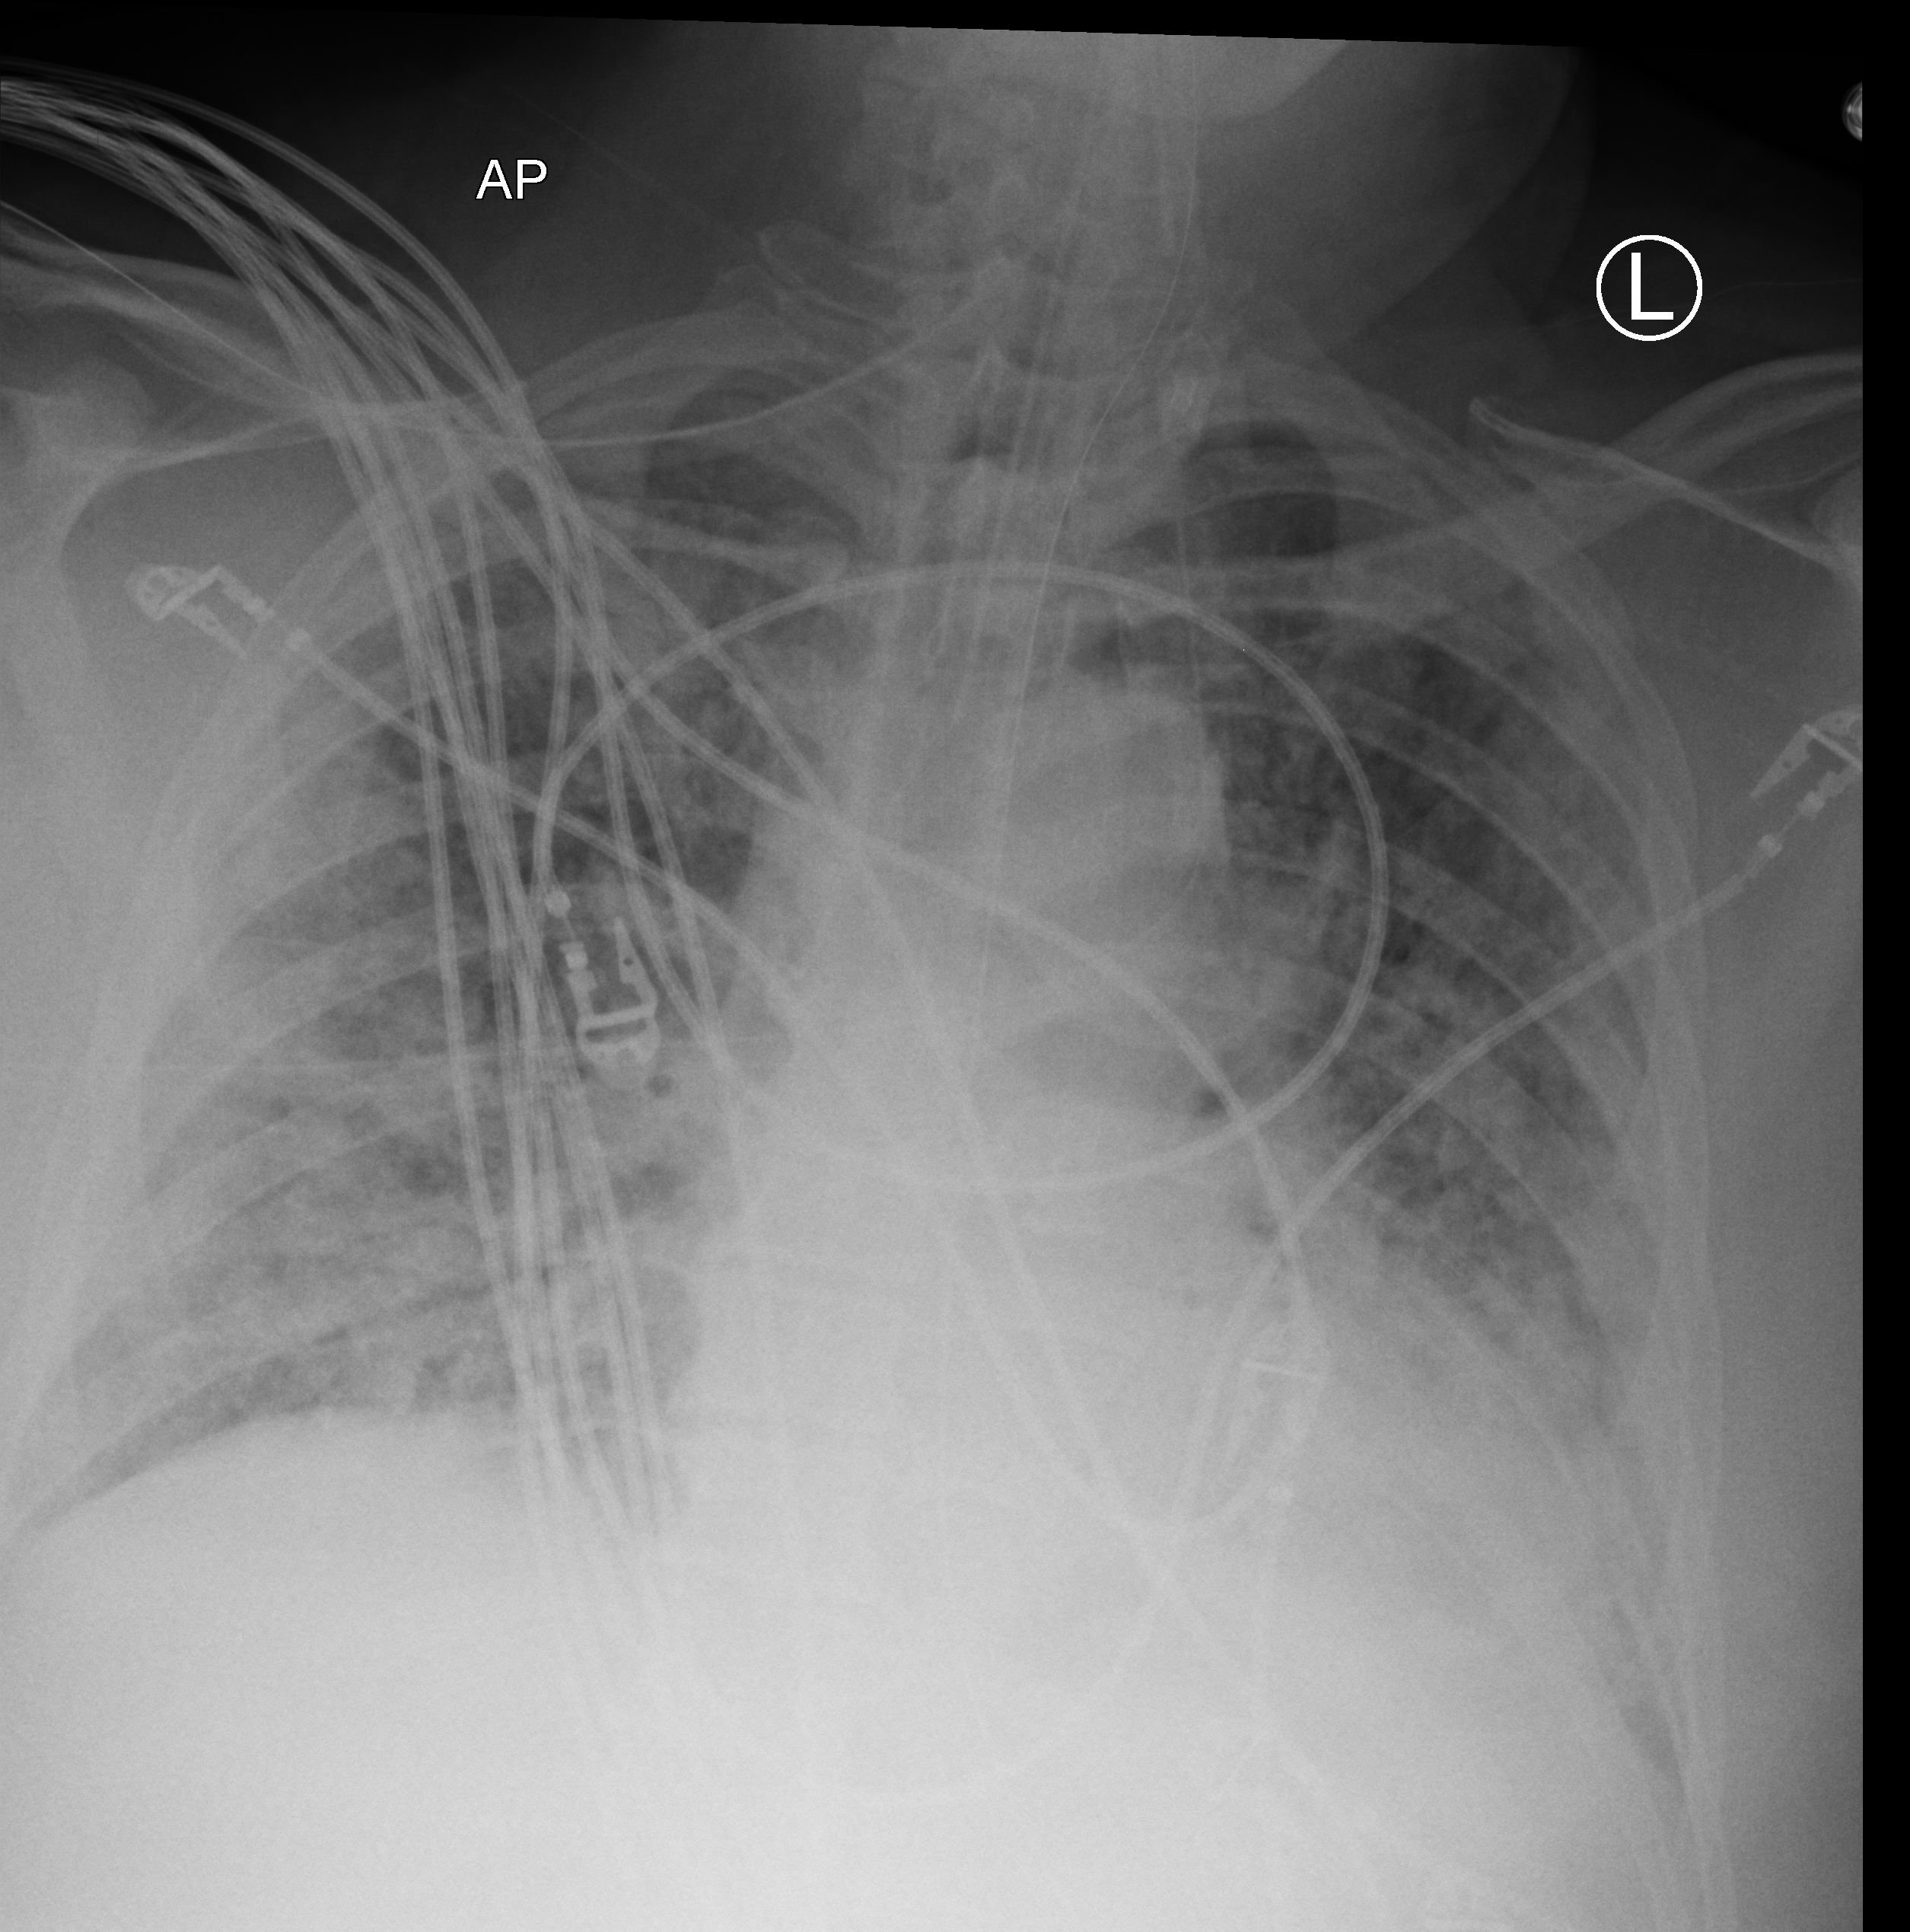
Chest X-ray (portable). Patient hospitalised with COVID-19; male, aged 60–74 years.
From the hospital-stay record, not from the radiograph (when in the stay this image was taken is not recorded): mechanically ventilated during this hospital stay: yes.